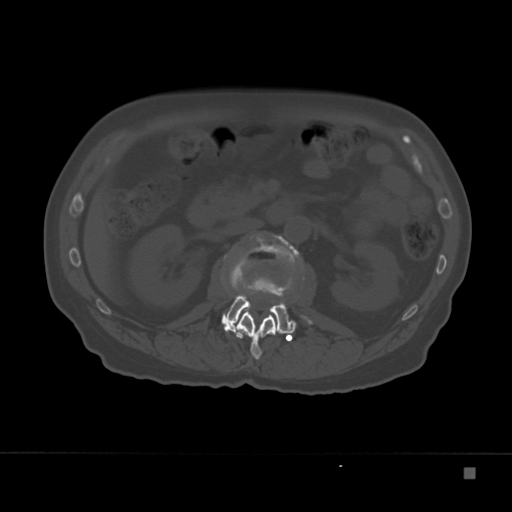
CT including the spine, one axial slice; slice 99 of 332 in the series (ordered by position); 120 kVp; bone window (W 1800 / L 400 HU); 512 × 512 image matrix. Patient: male, 72 years. Case-level facts recorded for this patient, not image findings: primary cancer: skeletal.
Annotated regions visible in this slice (semi-automatic segmentation, software-assisted and operator-edited):
- L1 vertebra: bounding box <229,262,284,360> (left, top, right, bottom; pixels)
- L2 vertebra: <222,243,312,334>